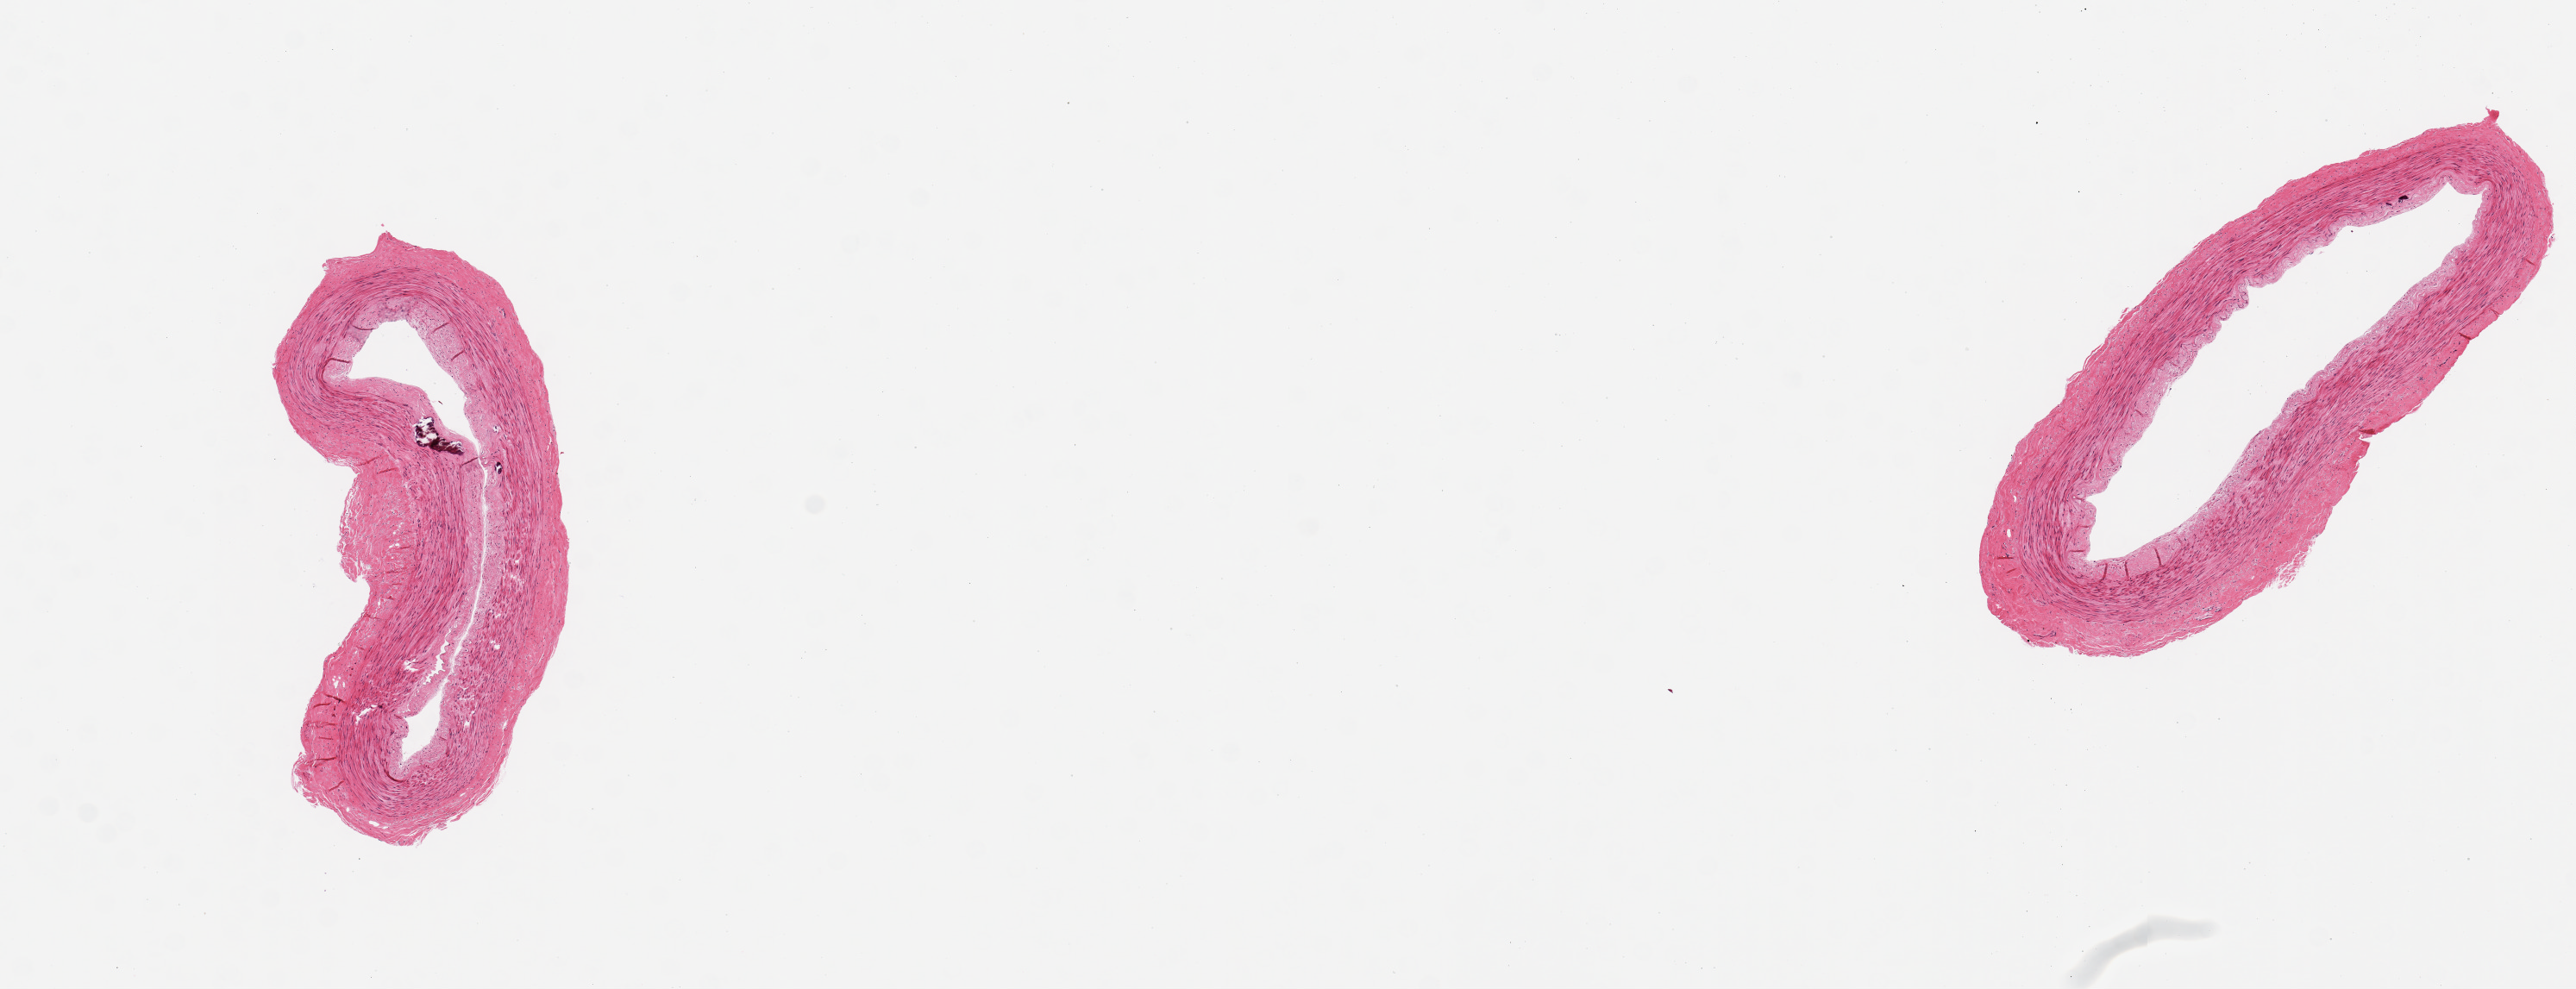
Whole-slide image, H&E stain, whole scanned area (about 11.8 x 4.5 mm) shown as a low-resolution overview; PAXgene-fixed paraffin-embedded (PFPE) section; section of tibial artery (target tissue); tissue donor sample.
Reviewer comment on this tissue sample: 2 pieces; minimal intimal thickening; calcific foci in 1 piece; well trimmed.